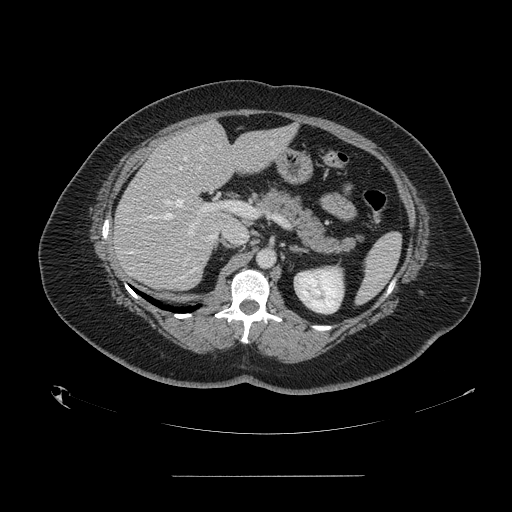
Contrast-enhanced abdominal CT, one axial slice. Position 87 of 164 along the scan axis. 120 kVp. Soft-tissue window (W 400 / L 40 HU). 512 × 512 image matrix, field of view 495 × 495 mm. Female patient, age 52 years. Case-level facts recorded for this patient, not image findings: diagnosis: colorectal cancer liver metastases, imaged before liver resection; multiple liver metastases: yes; largest metastasis: 3.5 cm; disease in both lobes: no.
Outlined on this slice (expert manual segmentation):
- hepatic veins: bounding box <164,142,273,219> (left, top, right, bottom; pixels)
- liver: <114,122,293,290>
- planned liver remnant (the part of the liver to remain after resection): <177,122,293,223>
- portal vein (with intrahepatic branches): <172,187,241,235>